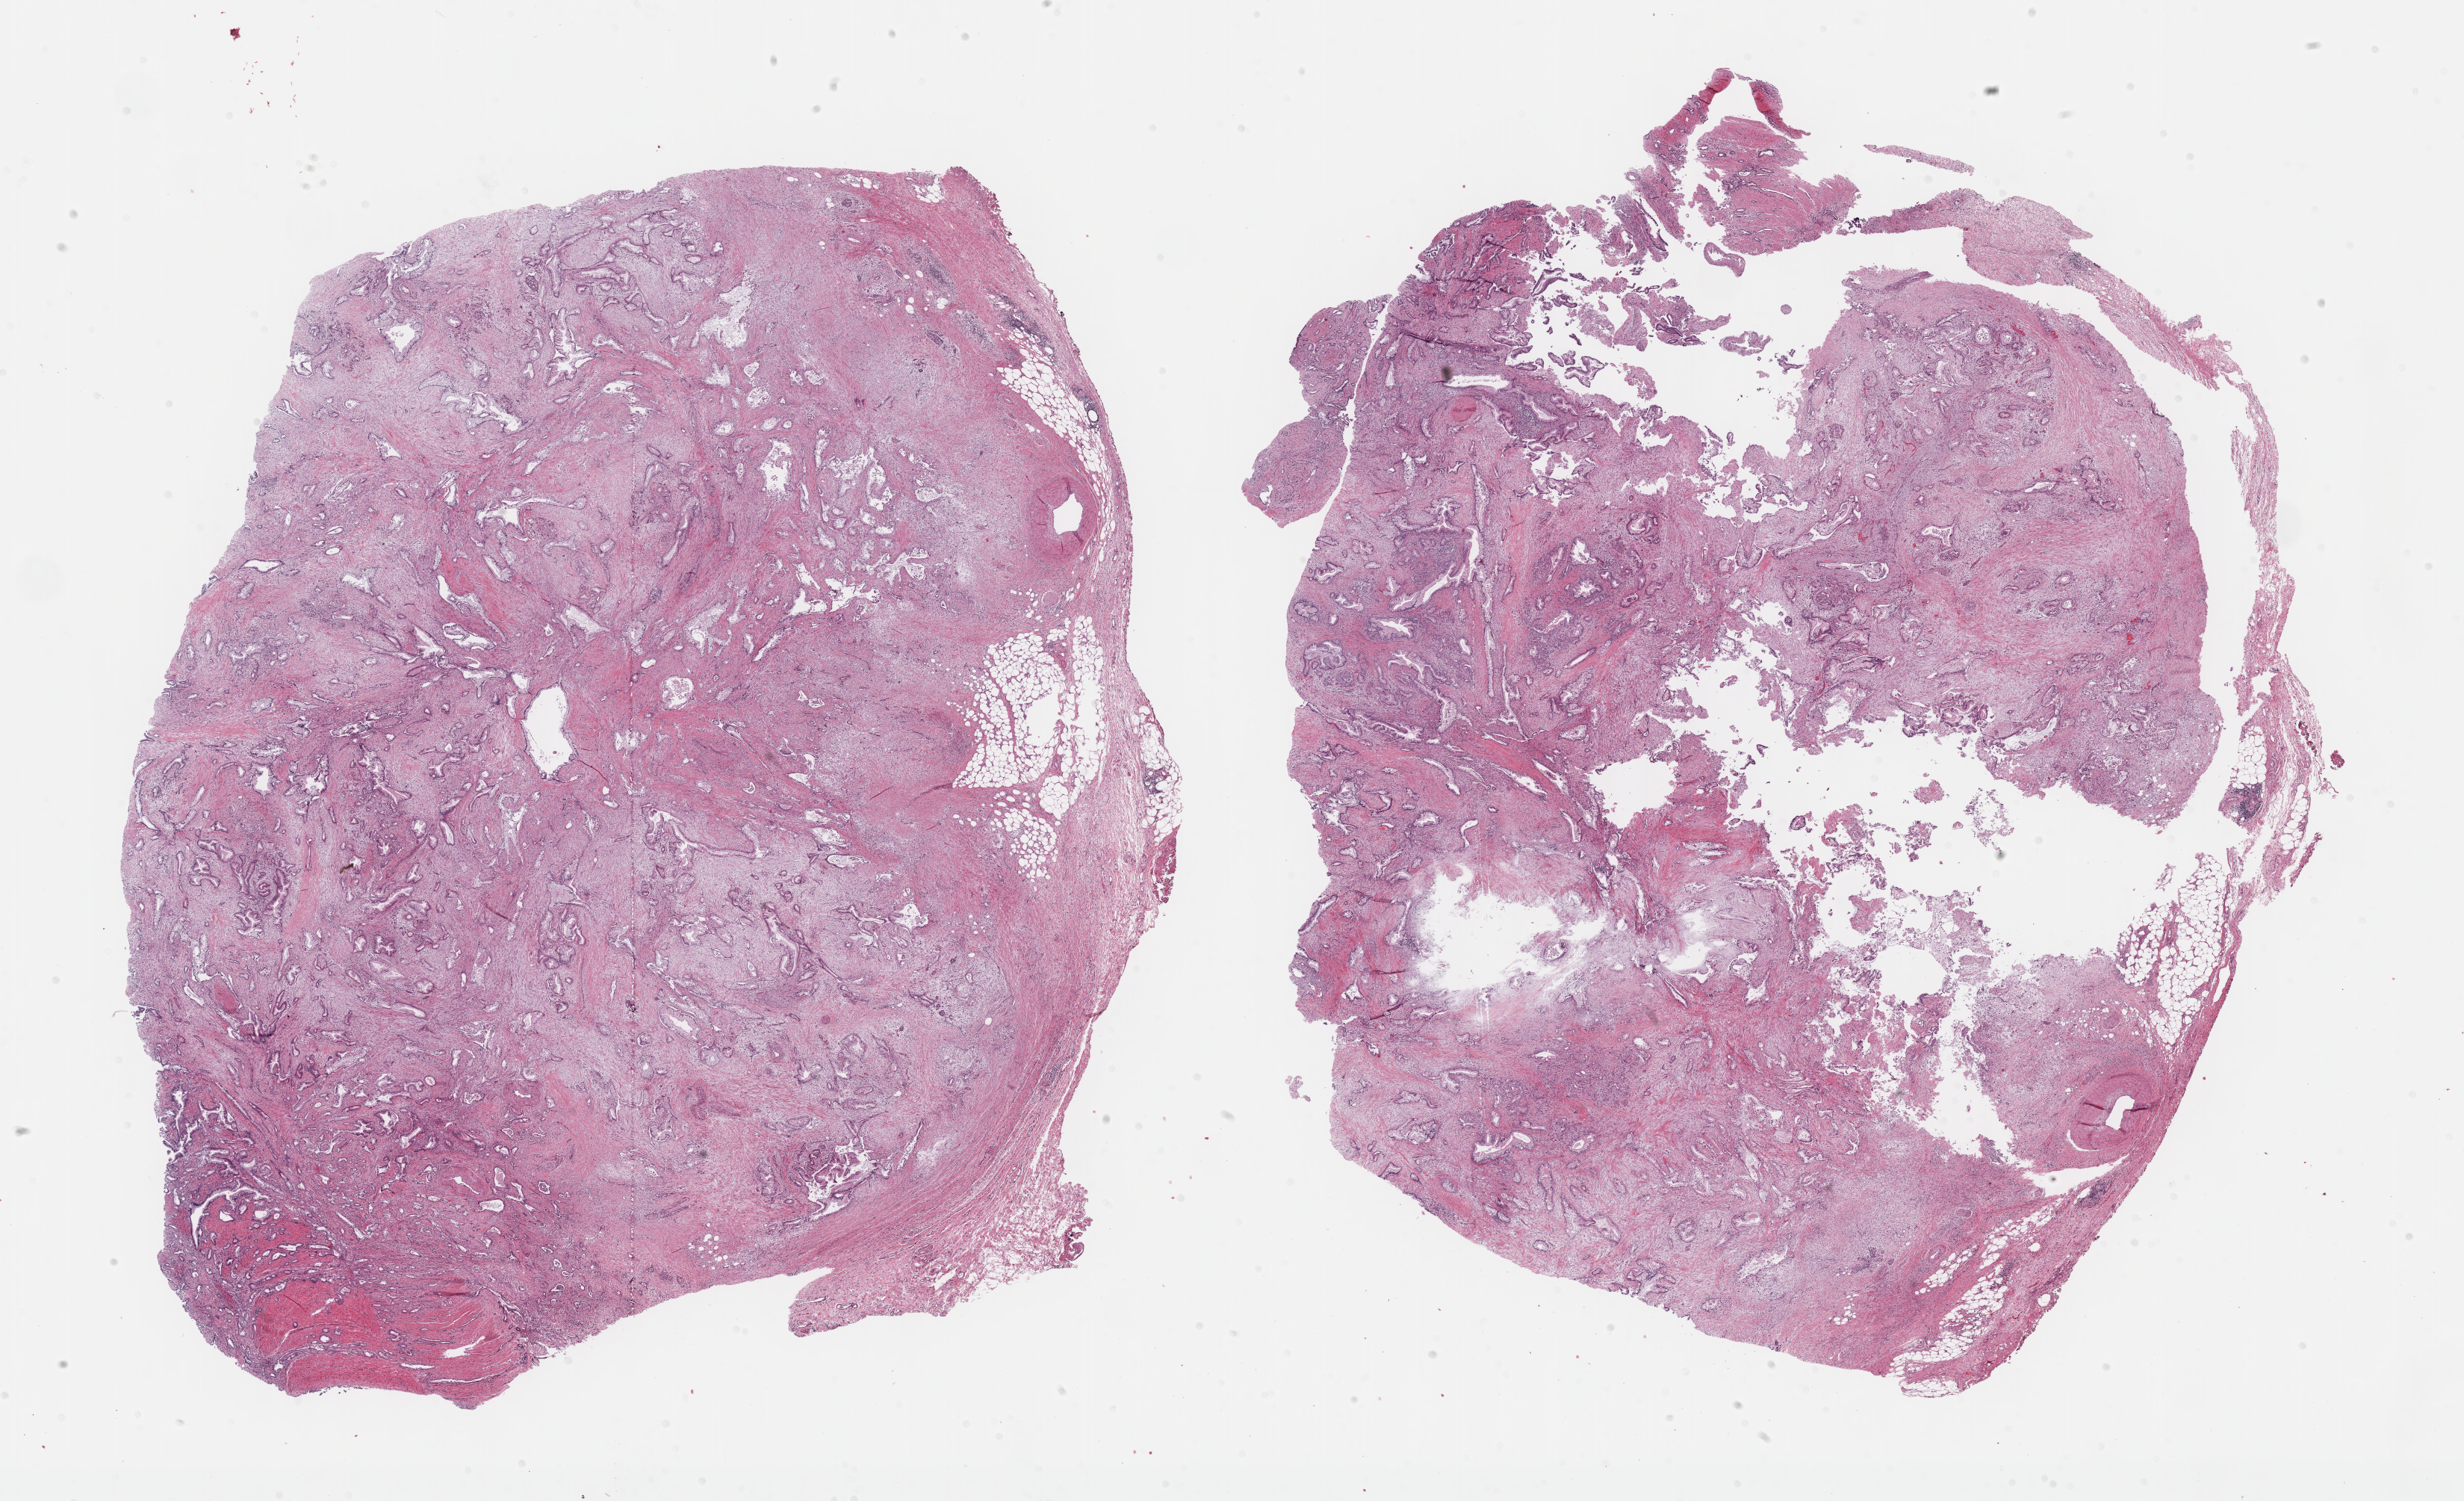
Digitized H&E tissue section (whole slide) — shown as a low-resolution overview of the whole scanned area (about 26.7 x 16.2 mm, slide scanned at 40x), FFPE section, primary tumour sample from the pancreas. Patient: female, age at initial diagnosis 72 years. Histologic grade: G2 (moderately differentiated).
AJCC pathologic stage: IIB (7th edition). Pathologic diagnosis: Infiltrating duct carcinoma, NOS (head of pancreas).